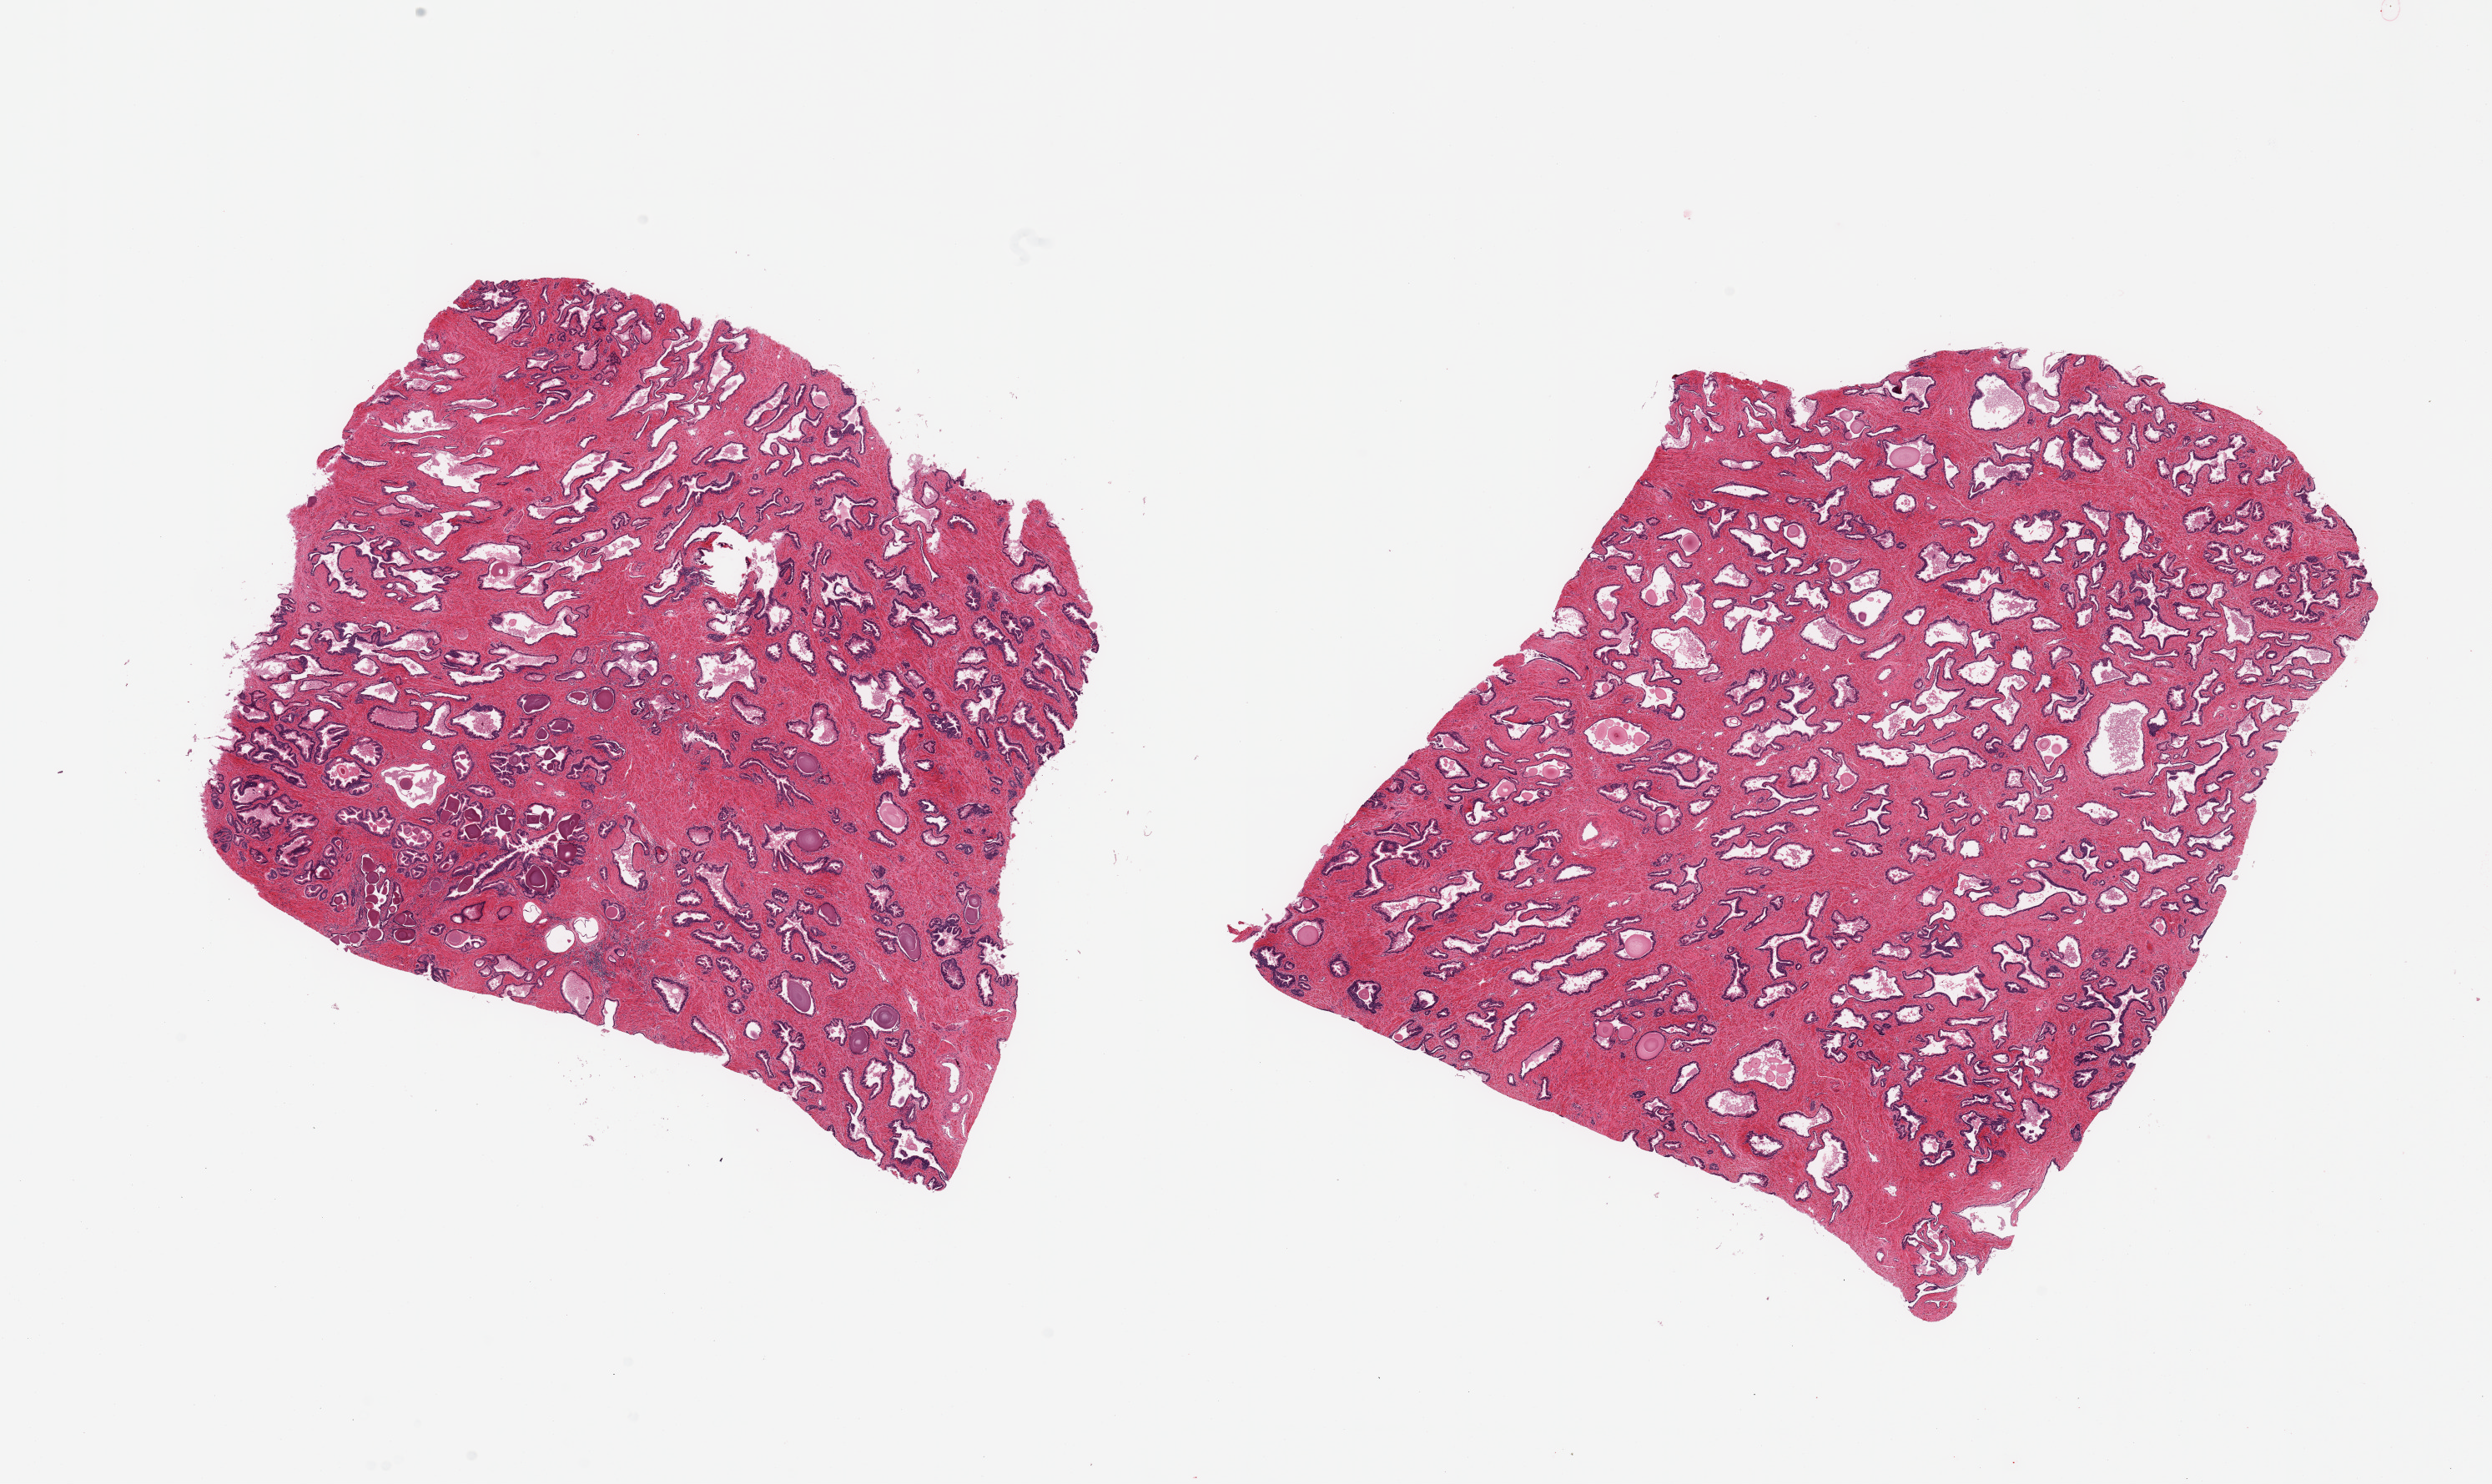
Whole-slide image, haematoxylin and eosin stain — a low-resolution overview of the entire scanned area, about 23.6 x 14.1 mm. PAXgene-fixed, paraffin-embedded tissue. Target tissue: prostate. Tissue donor sample. Donor sex: male.
Review note (as recorded): 2 pieces, hyperplastic glandular pattern.